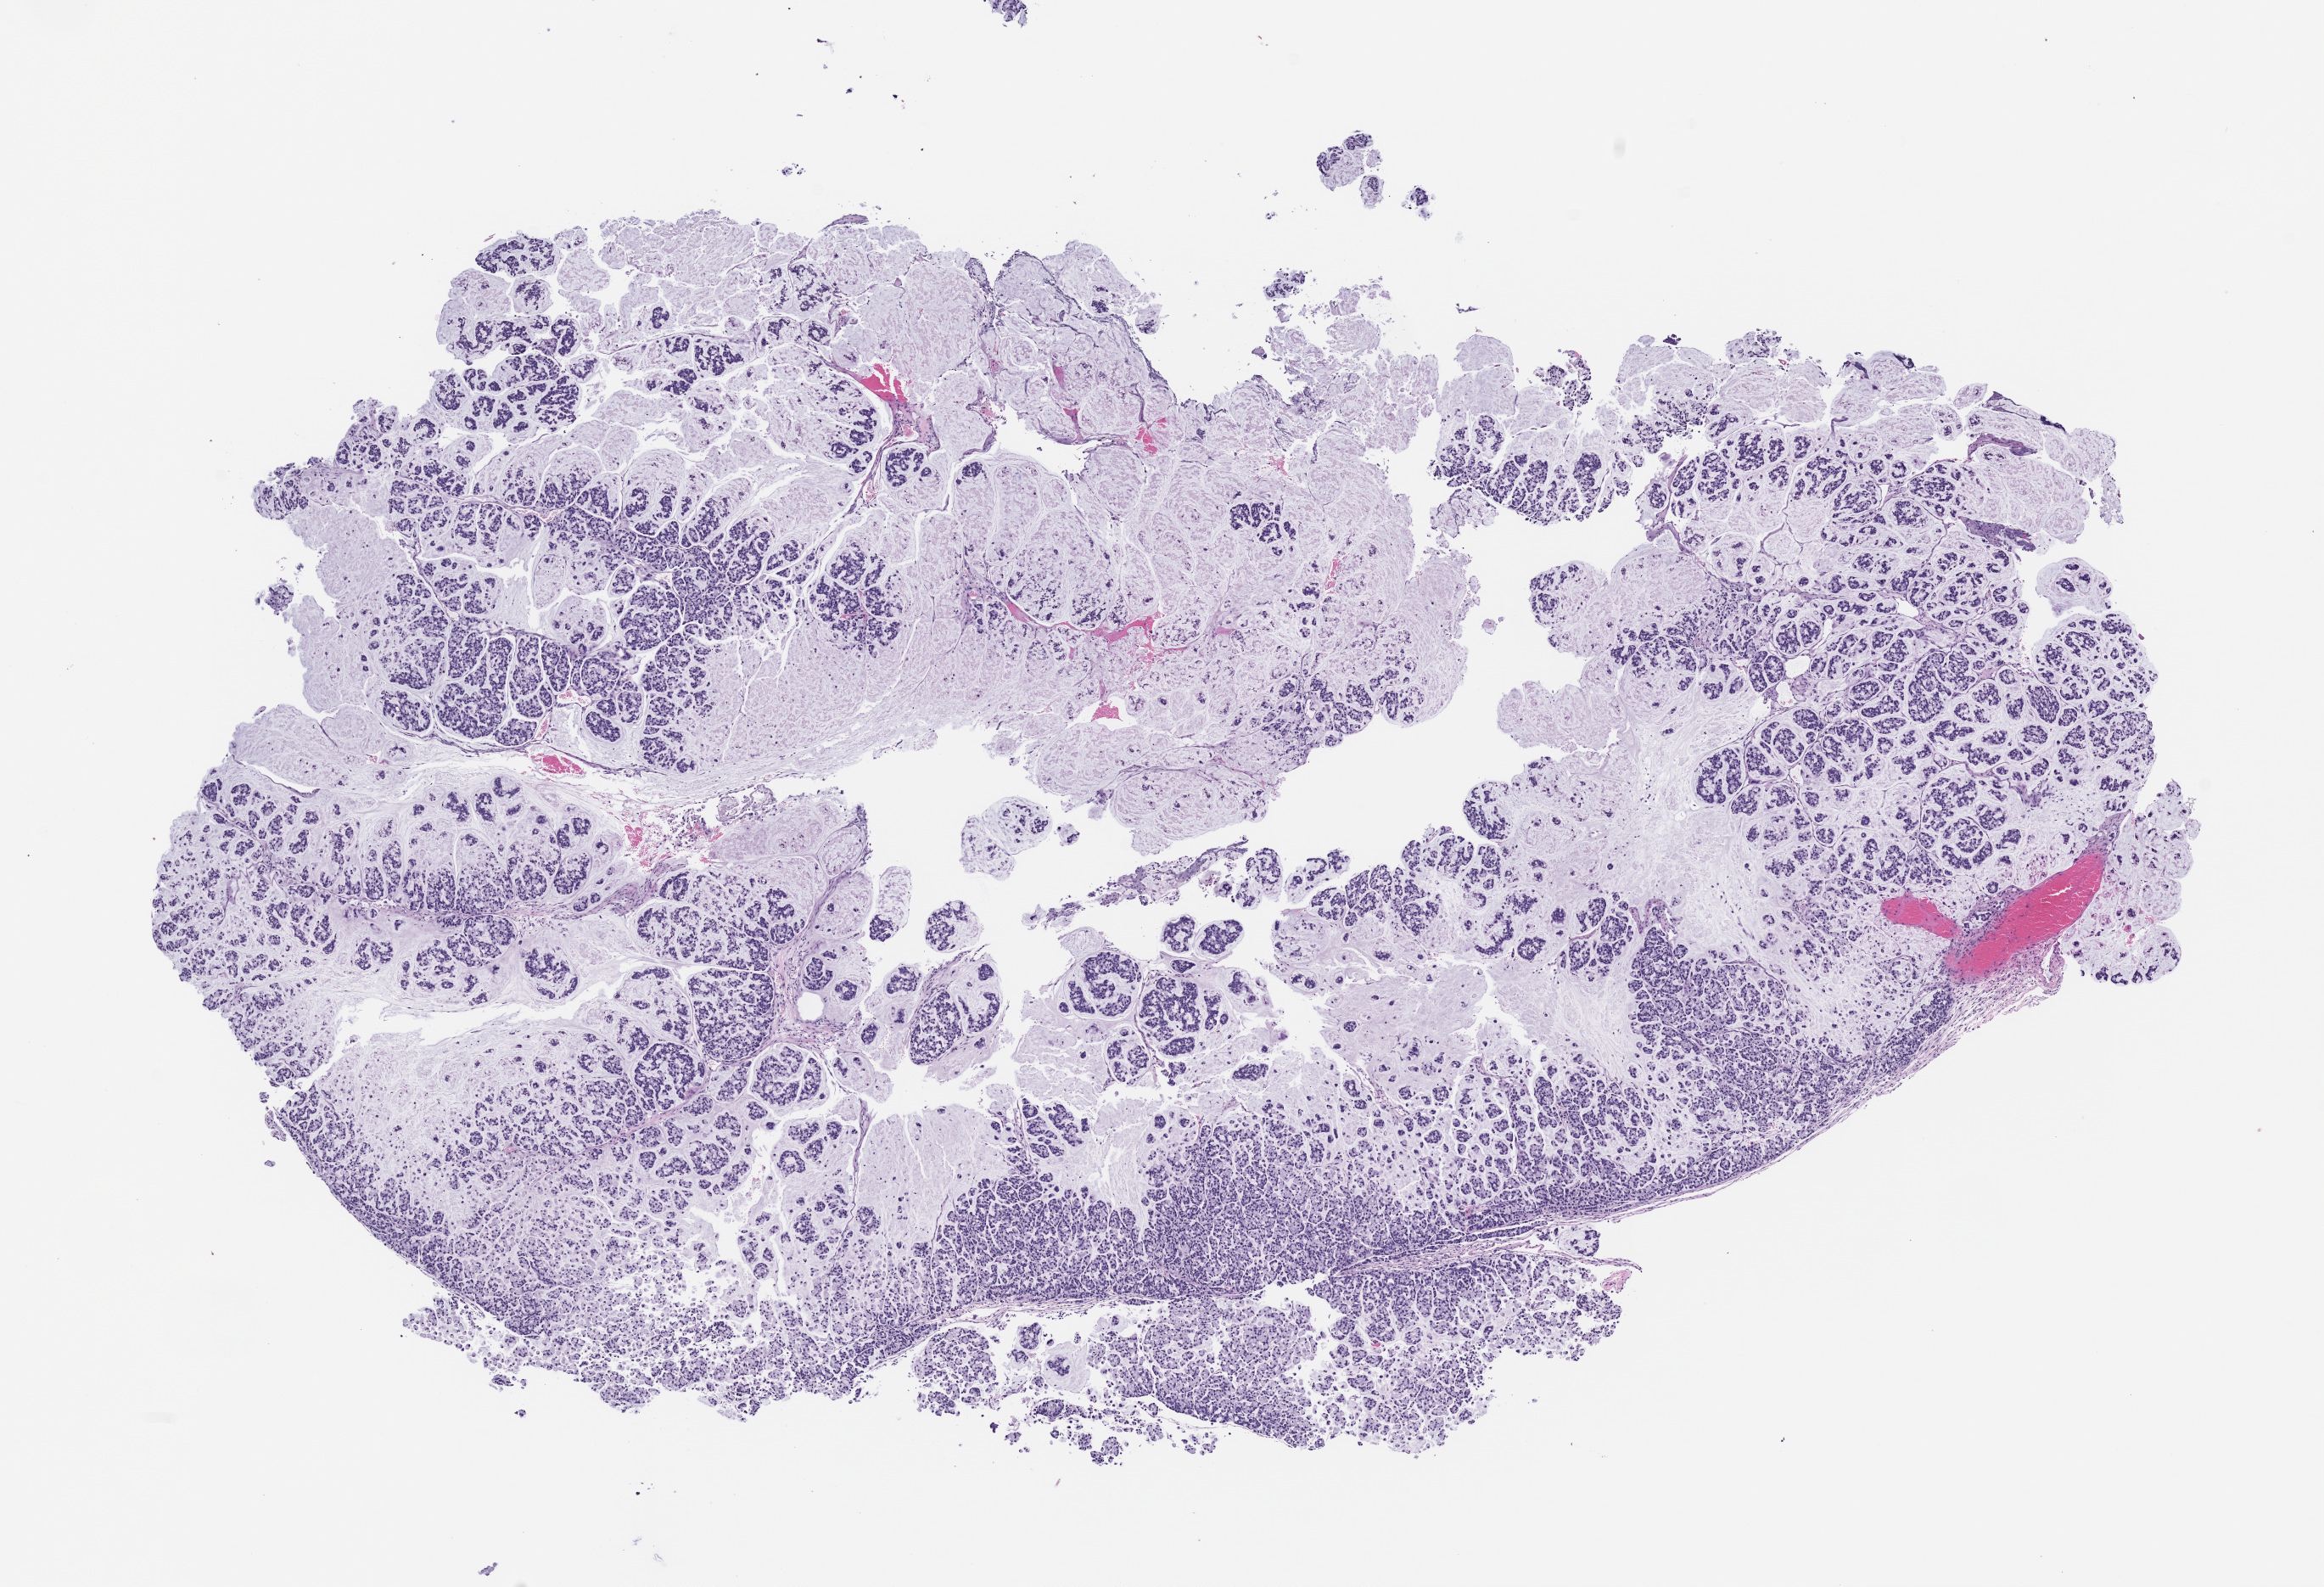
Haematoxylin and eosin whole-slide image of a patient-derived xenograft (PDX) tumor grown in a mouse, passage 0, whole scanned area (about 11.0 x 7.5 mm) shown as a low-resolution overview, formalin-fixed paraffin-embedded section, tumor site category: colon.
Originating patient diagnosis: Colon Adenocarcinoma.